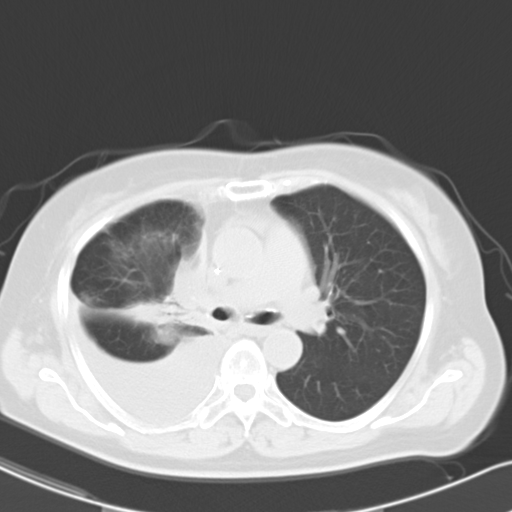
Chest CT, one axial slice; slice 17 of 26 in the series (ordered by position); reconstruction kernel B40f; 120 kVp; lung window (W 1500 / L -600 HU); 10 mm slice thickness; 512 × 512 image matrix, field of view 328 × 328 mm. Patient: female, 69 years. From the clinical record (not read from this slice): clinical TNM (as recorded): T2a N0 M1c.
Outlined on this slice (bounding box drawn by a radiologist):
- lung tumour (recorded histology: adenocarcinoma): bounding box [x1, y1, x2, y2] px = [134, 221, 213, 333]